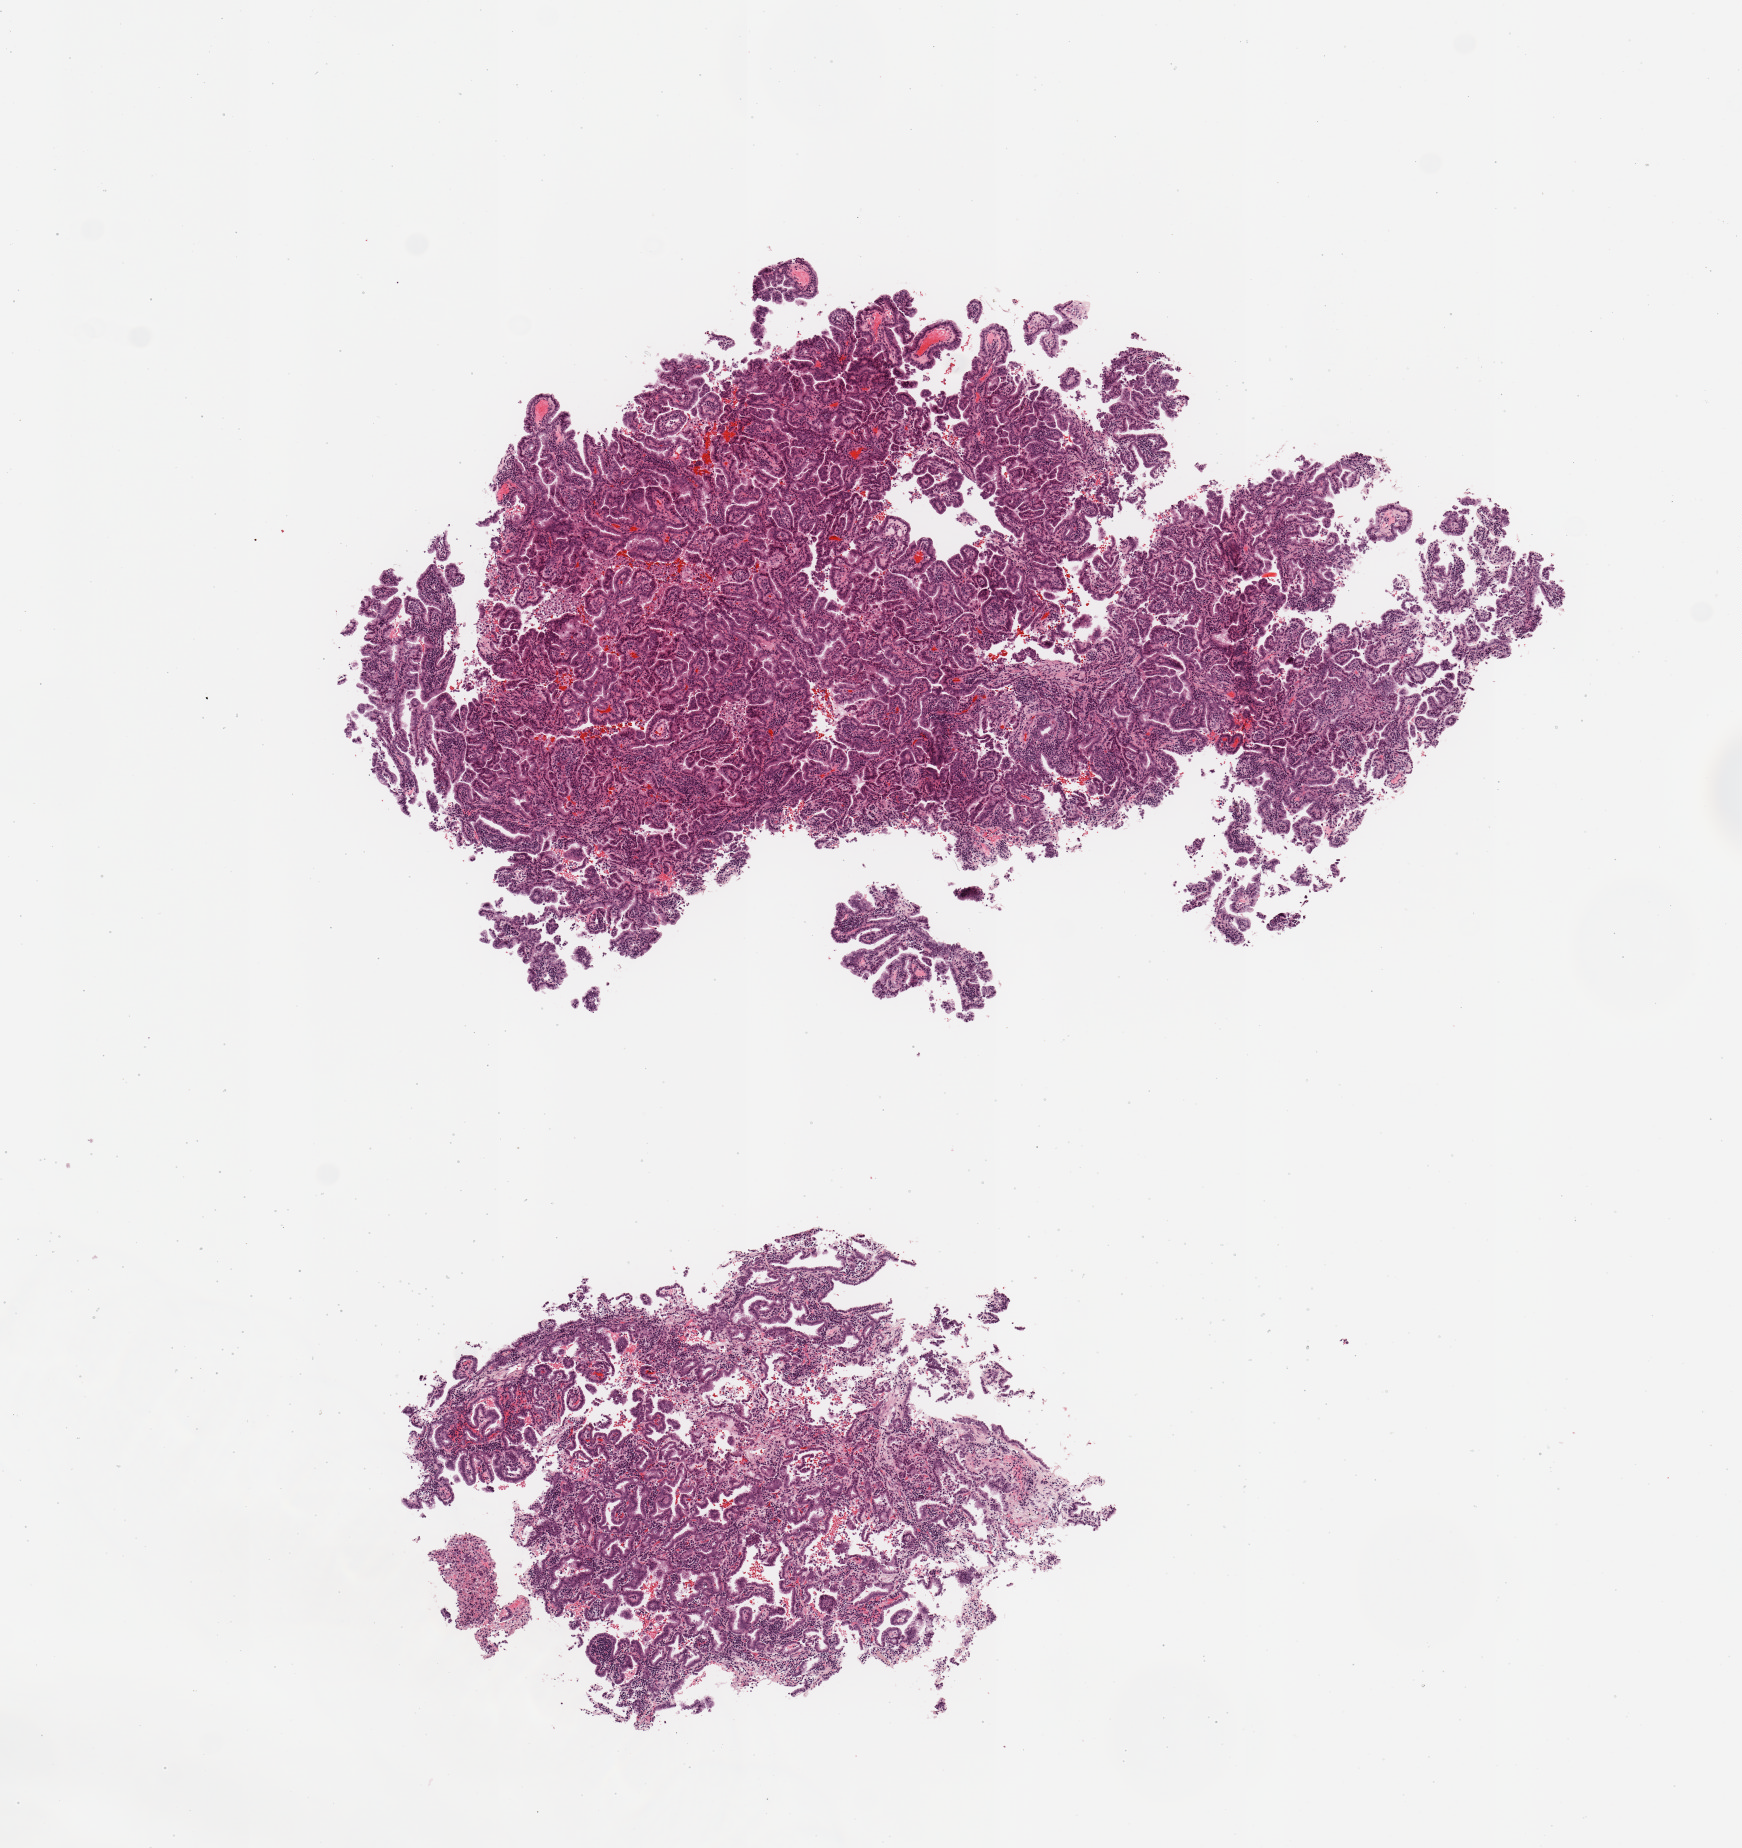
Digitized H&E tissue section (whole slide), shown as a low-resolution overview of the whole scanned area (about 6.9 x 7.3 mm, from a 20x scan), tumour tissue sample, sampled site: lung. Patient: male, age 74 years. Histologic grade: G1 (well differentiated). Composition of this section per pathologist review: tumour nuclei 80%, necrosis 5%.
AJCC pathologic stage: IA2. Diagnosis: Adenocarcinoma, NOS.